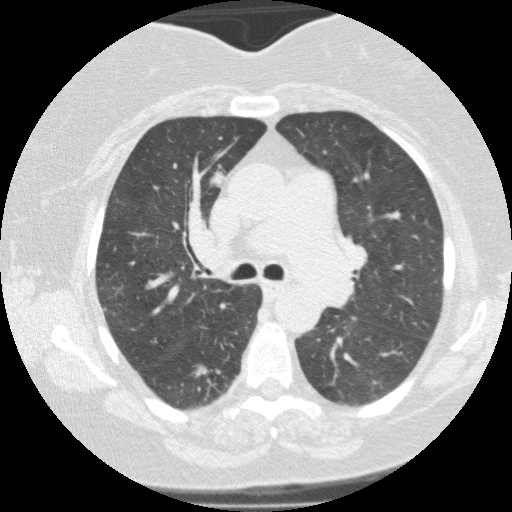
Low-dose screening chest CT, one axial slice. Position 92 of 146 along the scan axis. Reconstruction kernel FC01. Lung window (W 1500 / L -600 HU). 512 × 512 image matrix.
Outlined on this slice (manually delineated by an expert):
- lesion 2 (tumor, upper lobe of right lung): box from (x=210, y=171) to (x=225, y=188) px
- lesion 3 (nodule, lower lobe of right lung): (x=192, y=363)–(x=207, y=377)